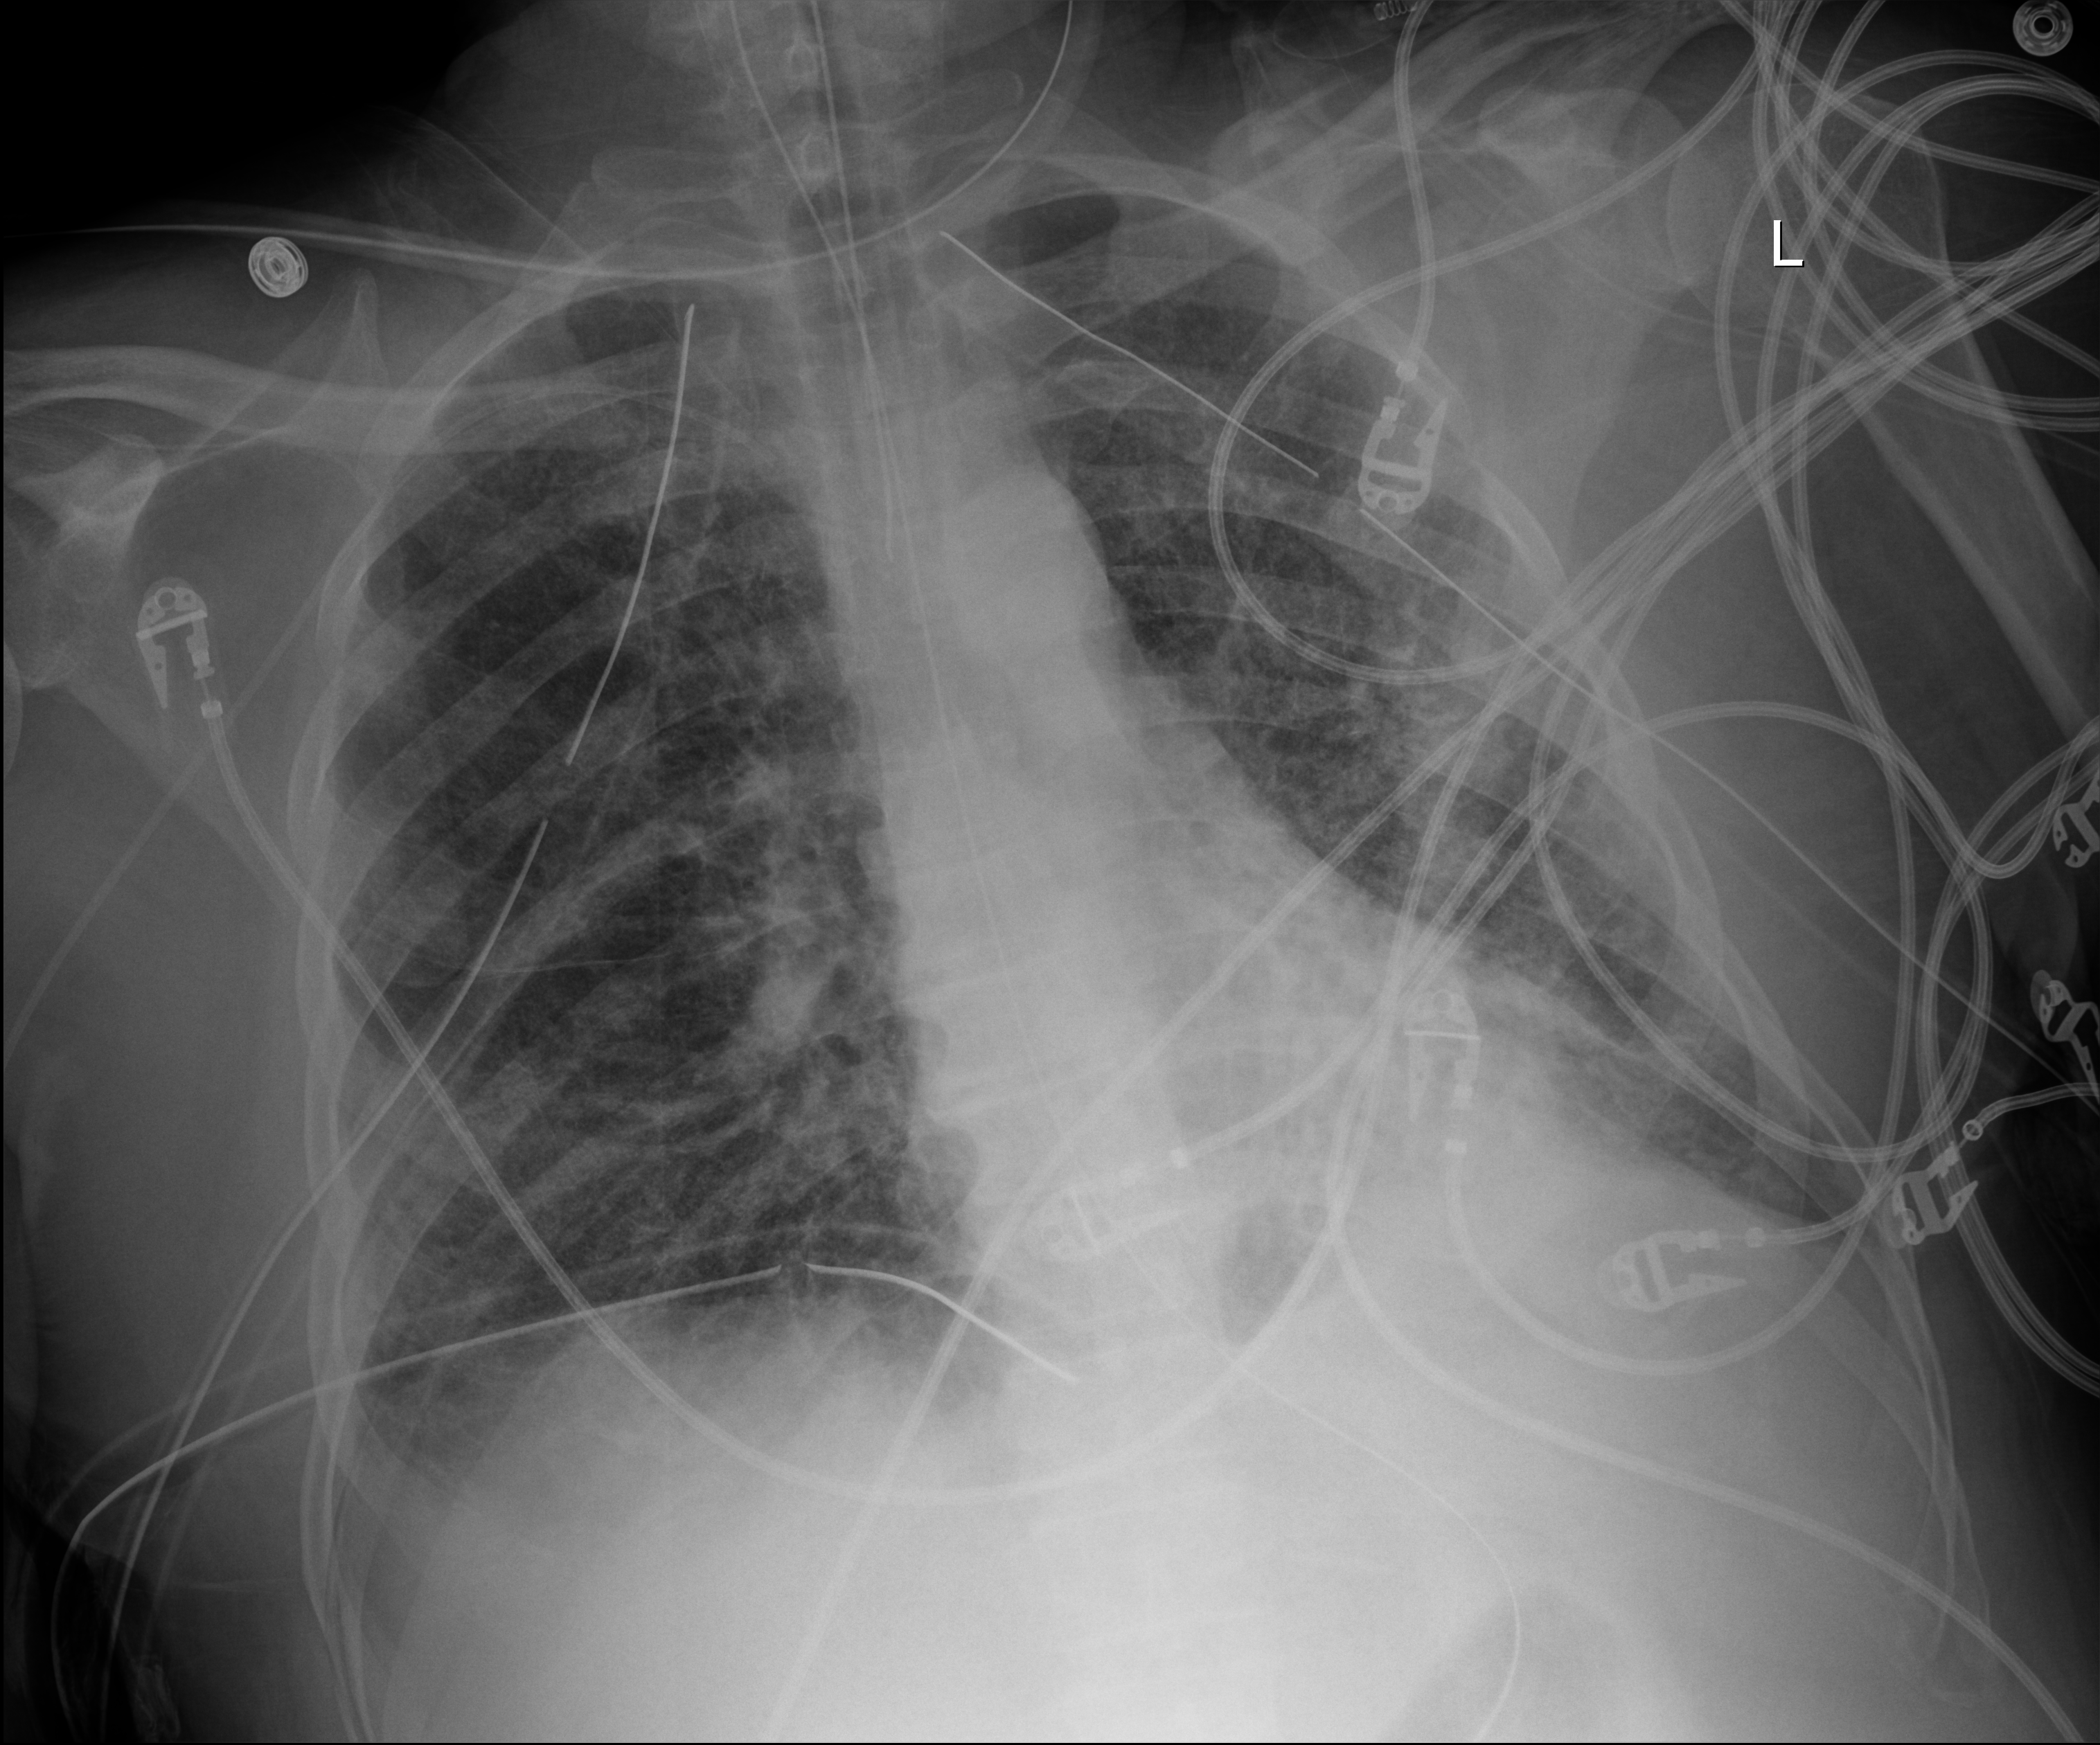
Portable chest radiograph, anteroposterior (AP) projection. Male patient hospitalised with COVID-19, age 18–59 years.
Admission-level facts for this patient (not findings on this image; timing relative to this image not recorded):
- chronic kidney disease (admission record): no
- diabetes (admission record): no